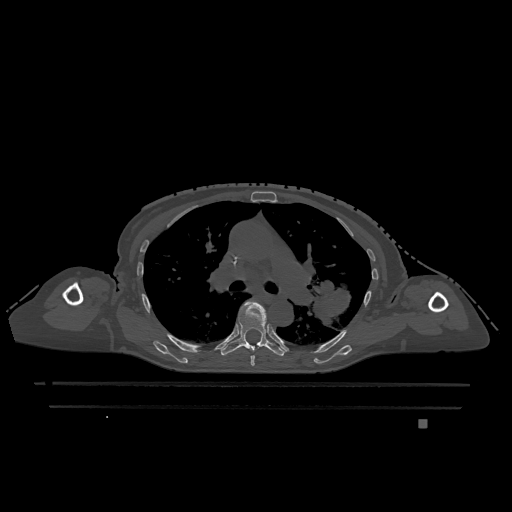
CT including the spine, one axial slice. Slice 804 of 1317 in the series (ordered by position). Bone window (W 1800 / L 400 HU). 512 × 512 image matrix. Female patient, age 74 years. From the clinical record (not read from this slice): primary cancer: lung.
Annotated regions visible in this slice (semi-automatically segmented with operator editing):
- T5 vertebra: box from (x=250, y=355) to (x=255, y=366) px
- T6 vertebra: (x=220, y=301)–(x=285, y=356)